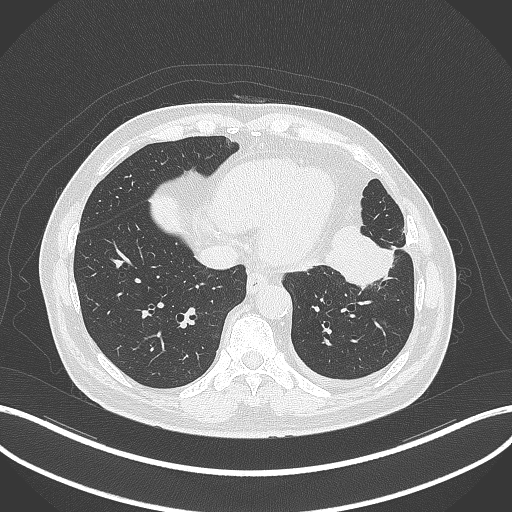
Chest CT, one axial slice. Position 103 of 230 along the scan axis. Reconstruction kernel B70f. 120 kVp. Lung window (W 1500 / L -600 HU). 1 mm slice thickness. 512 × 512 image matrix, field of view 400 × 400 mm. Male patient, age 68 years. From the clinical record (not read from this slice): clinical TNM (as recorded): T2b N0 M0.
Outlined on this slice (rectangle marked by the reading radiologist):
- lung tumour (recorded histology: squamous cell carcinoma): box from (x=323, y=221) to (x=398, y=295) px